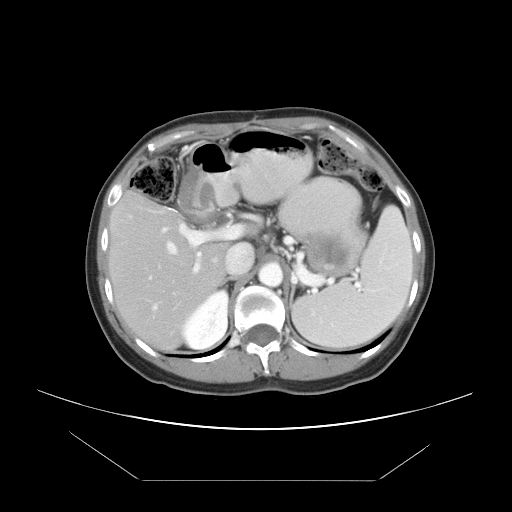
Contrast-enhanced abdominal CT, one axial slice; position 29 of 45 along the scan axis; reconstruction kernel STANDARD; 120 kVp; intravenous contrast given; soft-tissue window (W 400 / L 40 HU); 5 mm slice thickness; 512 × 512 image matrix, field of view 405 × 405 mm. Female patient, age 52 years. From the clinical record (not read from this slice): diagnosis: colorectal cancer liver metastases, imaged before liver resection; multiple liver metastases: yes; largest metastasis: 2.5 cm; disease in both lobes: no.
Annotated regions visible in this slice (manually delineated by an expert):
- hepatic veins: bounding box [x1, y1, x2, y2] px = [149, 243, 176, 310]
- liver: [110, 195, 227, 349]
- planned liver remnant (the part of the liver to remain after resection): [111, 195, 227, 344]
- portal vein (with intrahepatic branches): [162, 223, 232, 273]